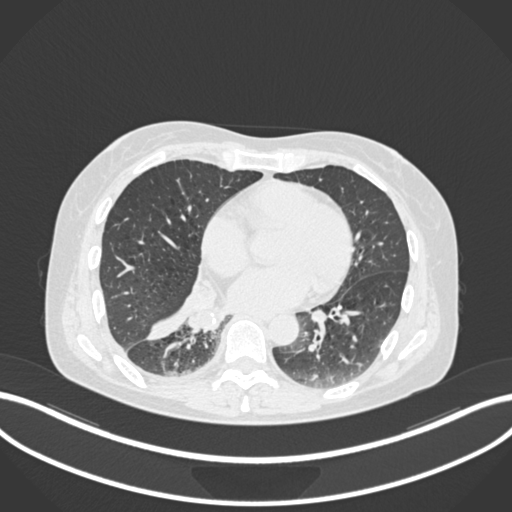
Chest CT, one axial slice. Slice 64 of 168 in the series (ordered by position). Reconstruction kernel B30f. 120 kVp. Lung window (W 1500 / L -600 HU). 1 mm slice thickness. 512 × 512 image matrix, field of view 400 × 400 mm. Patient: female, 63 years. From the clinical record (not read from this slice): clinical TNM (as recorded): T1c N0 M0.
Annotated regions visible in this slice (bounding box drawn by a radiologist):
- lung tumour (recorded histology: adenocarcinoma): bounding box [x1, y1, x2, y2] px = [182, 301, 229, 333]